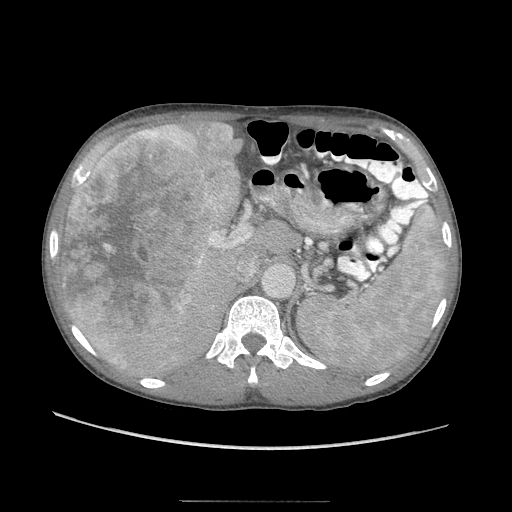
Contrast-enhanced abdominal CT (liver protocol), one axial slice. Position 60 of 103 along the scan axis. Reconstruction kernel STANDARD. Soft-tissue window (W 400 / L 40 HU). 512 × 512 image matrix, field of view 380 × 380 mm. Case-level facts recorded for this patient, not image findings: diagnosis: hepatocellular carcinoma (patient treated with transarterial chemoembolisation; whether this scan precedes or follows treatment is not stated here); TNM stage (as recorded): Stage-IIIA; Child-Pugh class: A; tumour differentiation: moderately differentiated.
Annotated regions visible in this slice (semi-automatic segmentation, software-assisted and operator-edited):
- liver parenchyma outside the tumour (the mass and vessels are separate outlines, so this box may not span the whole liver): bounding box [x1, y1, x2, y2] px = [56, 117, 264, 376]
- mass: [59, 123, 240, 367]
- liver vessels: [95, 218, 226, 354]